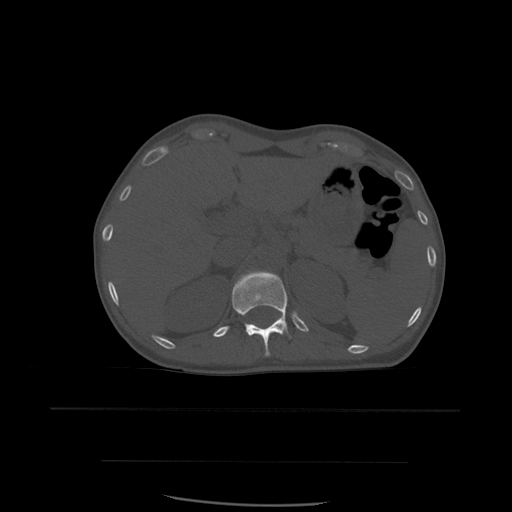
CT including the spine, one axial slice. Slice 272 of 574 in the series (ordered by position). Bone window (W 1800 / L 400 HU). 512 × 512 image matrix, field of view 392 × 392 mm. Patient age 48 years. From the clinical record (not read from this slice): primary cancer: lung; vertebrae with lytic lesions (as recorded): T11.
Structures marked on this image (semi-automatic segmentation, software-assisted and operator-edited):
- T12 vertebra: bounding box (x1, y1, x2, y2) in pixels: (232, 271, 291, 357)